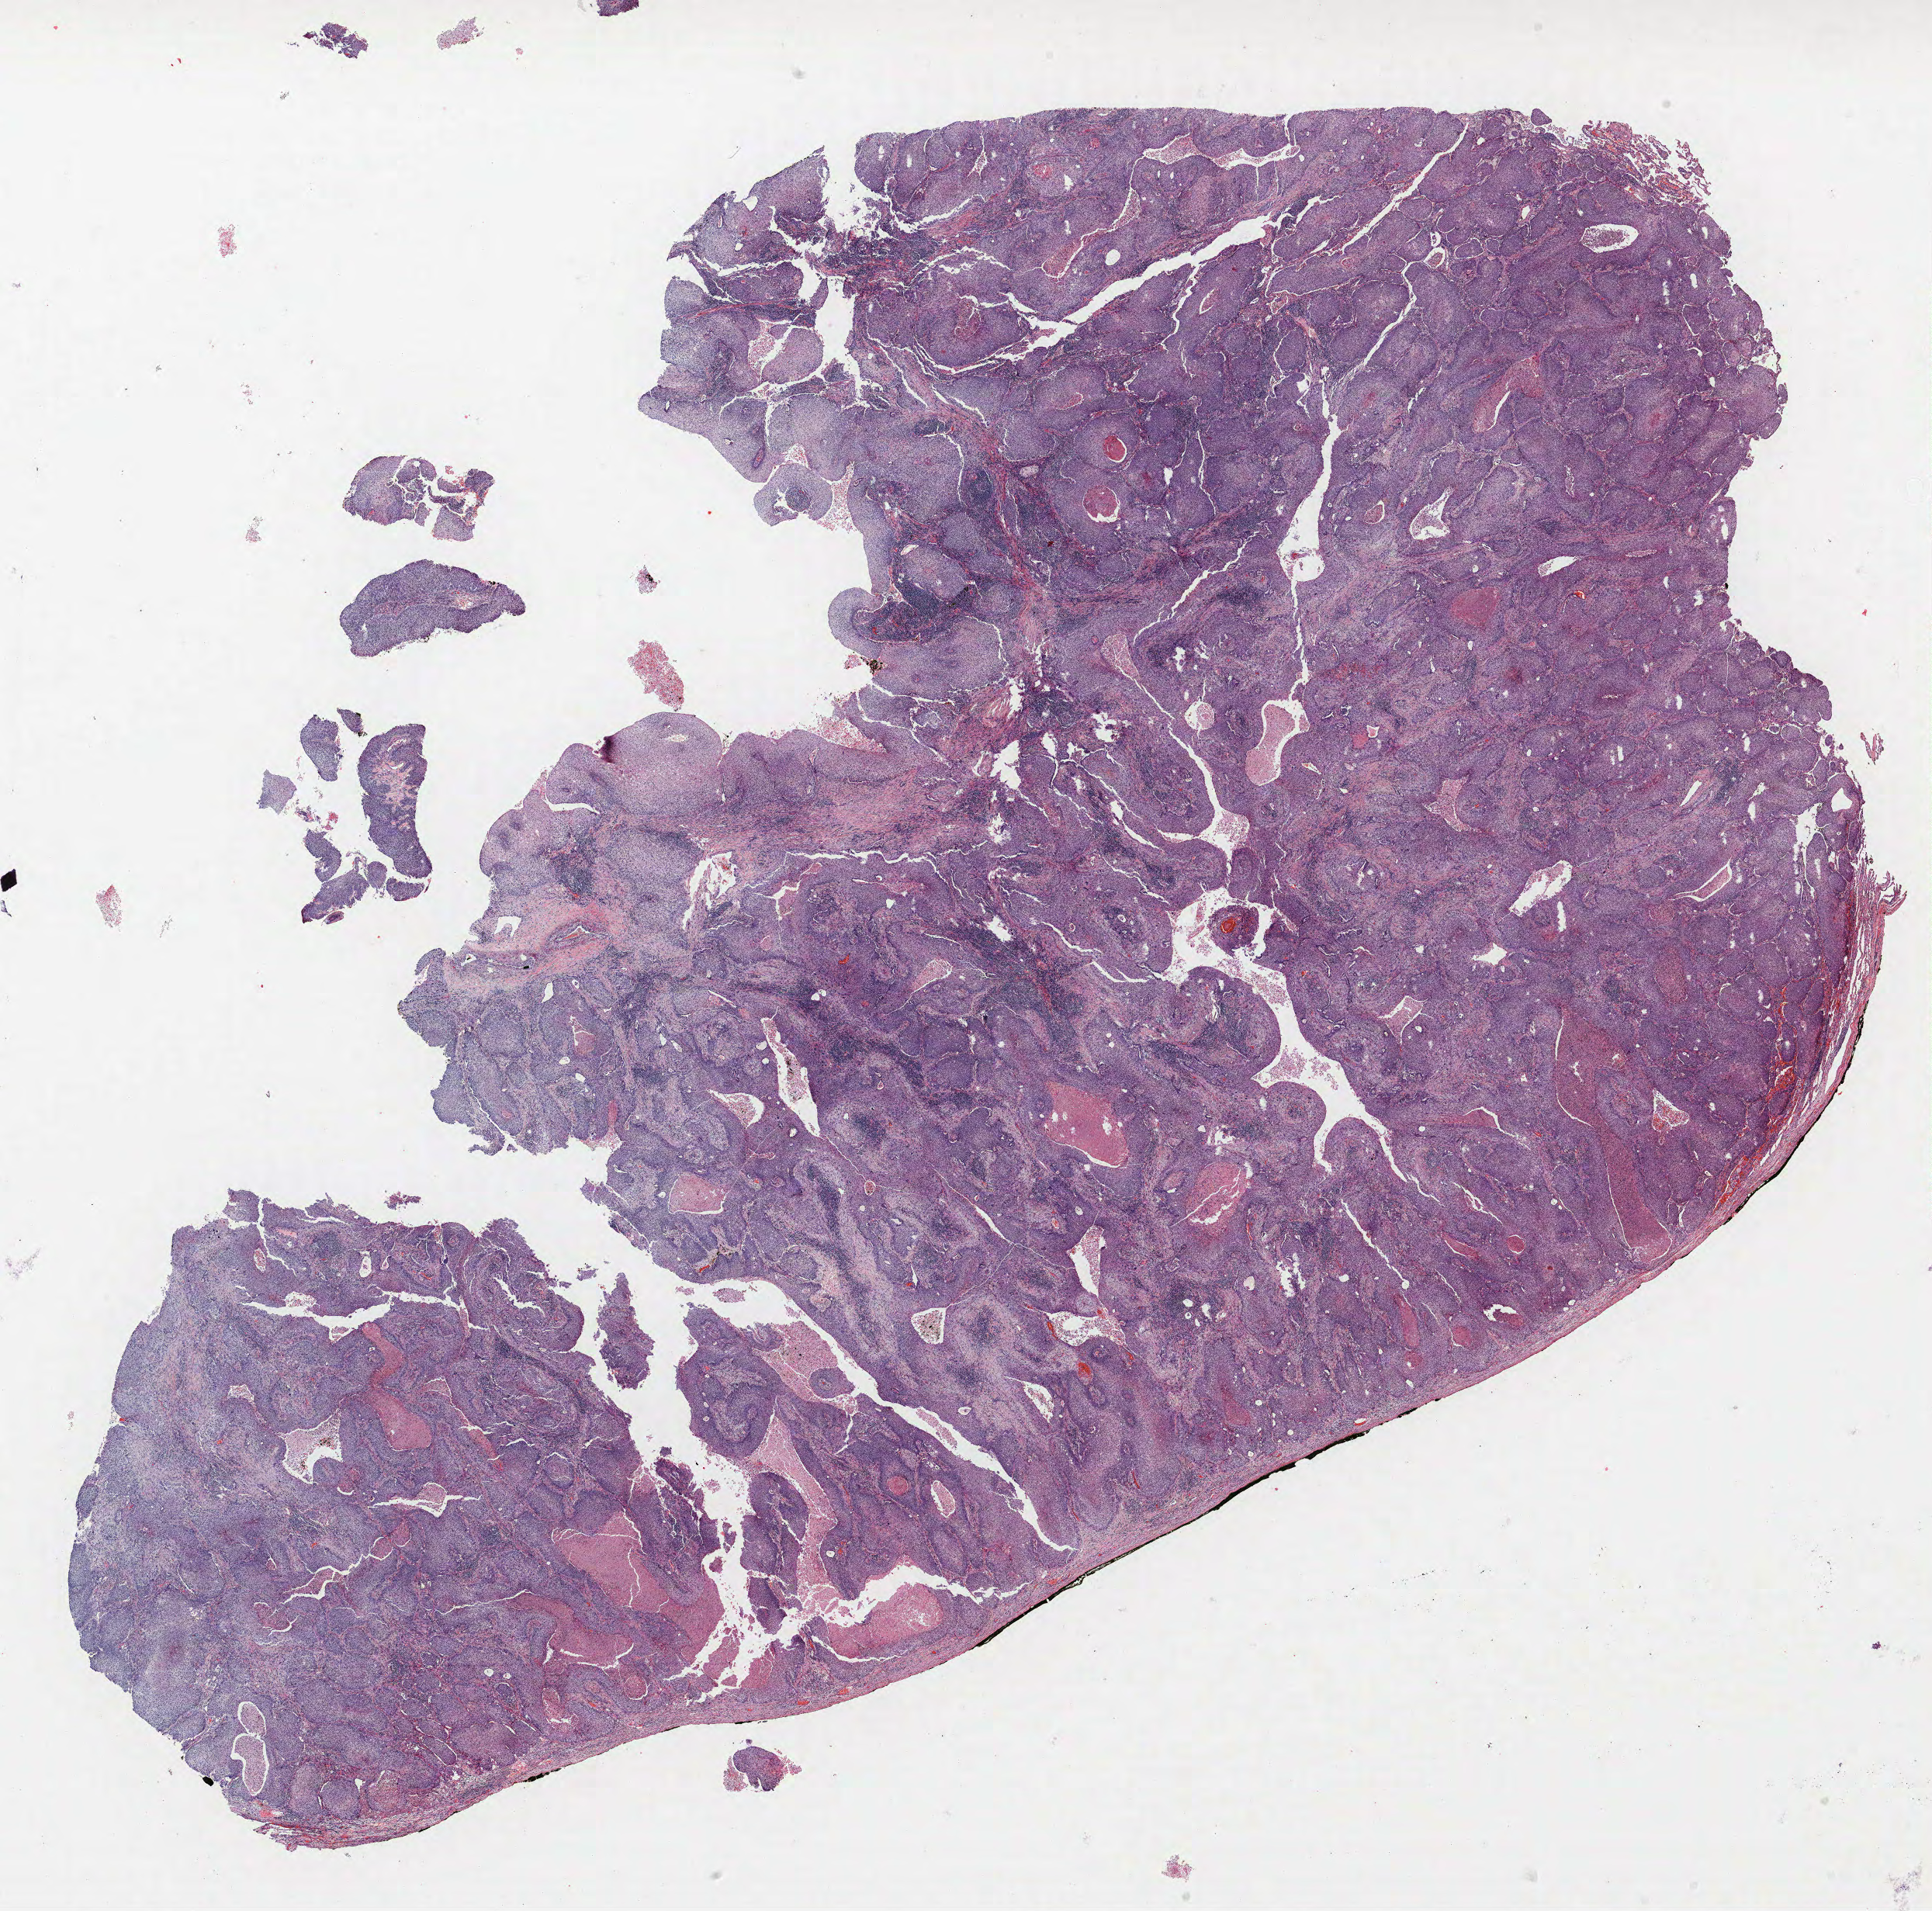
Whole-slide histology image, Hematoxylin and eosin (H&E) stained, a low-resolution overview of the entire scanned area, about 19.9 x 19.7 mm; FFPE section; lung. Male patient, aged 59 at enrolment. Current smoker at enrolment.
Participant's lung-cancer diagnosis: Adenocarcinoma, NOS. Note: participant had 2 primary lung cancers recorded; fields above describe the first.